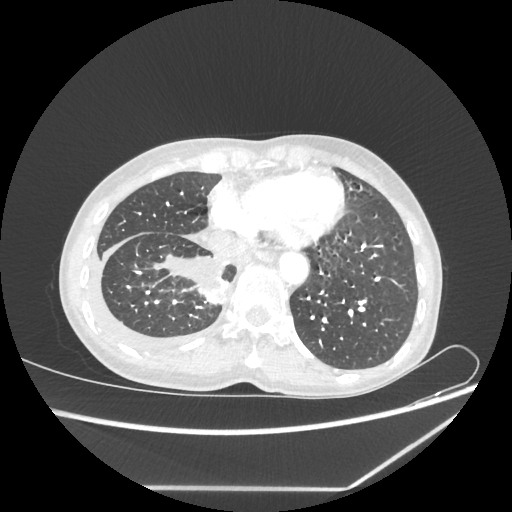
Chest CT, one axial slice; slice 62 of 237 in the series (ordered by position); reconstruction kernel STANDARD; 80 kVp; lung window (W 1500 / L -600 HU); 1.25 mm slice thickness; 512 × 512 image matrix. Female patient, age 59 years. Case-level facts recorded for this patient, not image findings: clinical TNM (as recorded): T1c N1 M1.
Outlined on this slice (bounding box drawn by a radiologist):
- lung tumour (recorded histology: adenocarcinoma): bounding box [x1, y1, x2, y2] px = [198, 274, 228, 308]